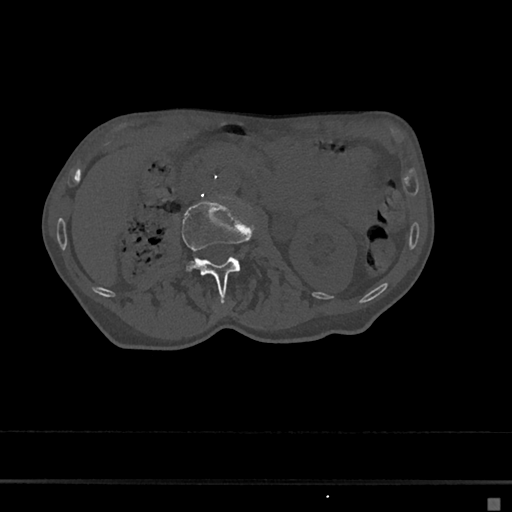
CT including the spine, one axial slice; slice 8 of 797 in the series (ordered by position); reconstruction kernel Br40s/3; 120 kVp; bone window (W 1800 / L 400 HU); 0.5 mm slice thickness; 512 × 512 image matrix. Female patient, age 68 years. Case-level facts recorded for this patient, not image findings: primary cancer: renal.
Outlined on this slice (semi-automatic segmentation, software-assisted and operator-edited):
- L2 vertebra: bounding box [x1, y1, x2, y2] px = [182, 199, 257, 296]